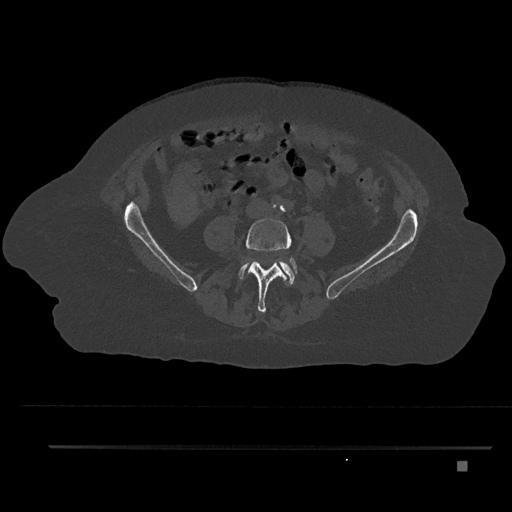
CT including the spine, one axial slice; slice 73 of 797 in the series (ordered by position); bone window (W 1800 / L 400 HU); 512 × 512 image matrix, field of view 437 × 437 mm. Patient: female, 76 years. Case-level facts recorded for this patient, not image findings: primary cancer: lung; vertebrae with lytic lesions (as recorded): T11, L3.
Annotated regions visible in this slice (semi-automatic segmentation, software-assisted and operator-edited):
- L4 vertebra: box from (x=241, y=218) to (x=298, y=313) px
- L5 vertebra: (x=238, y=259)–(x=296, y=286)